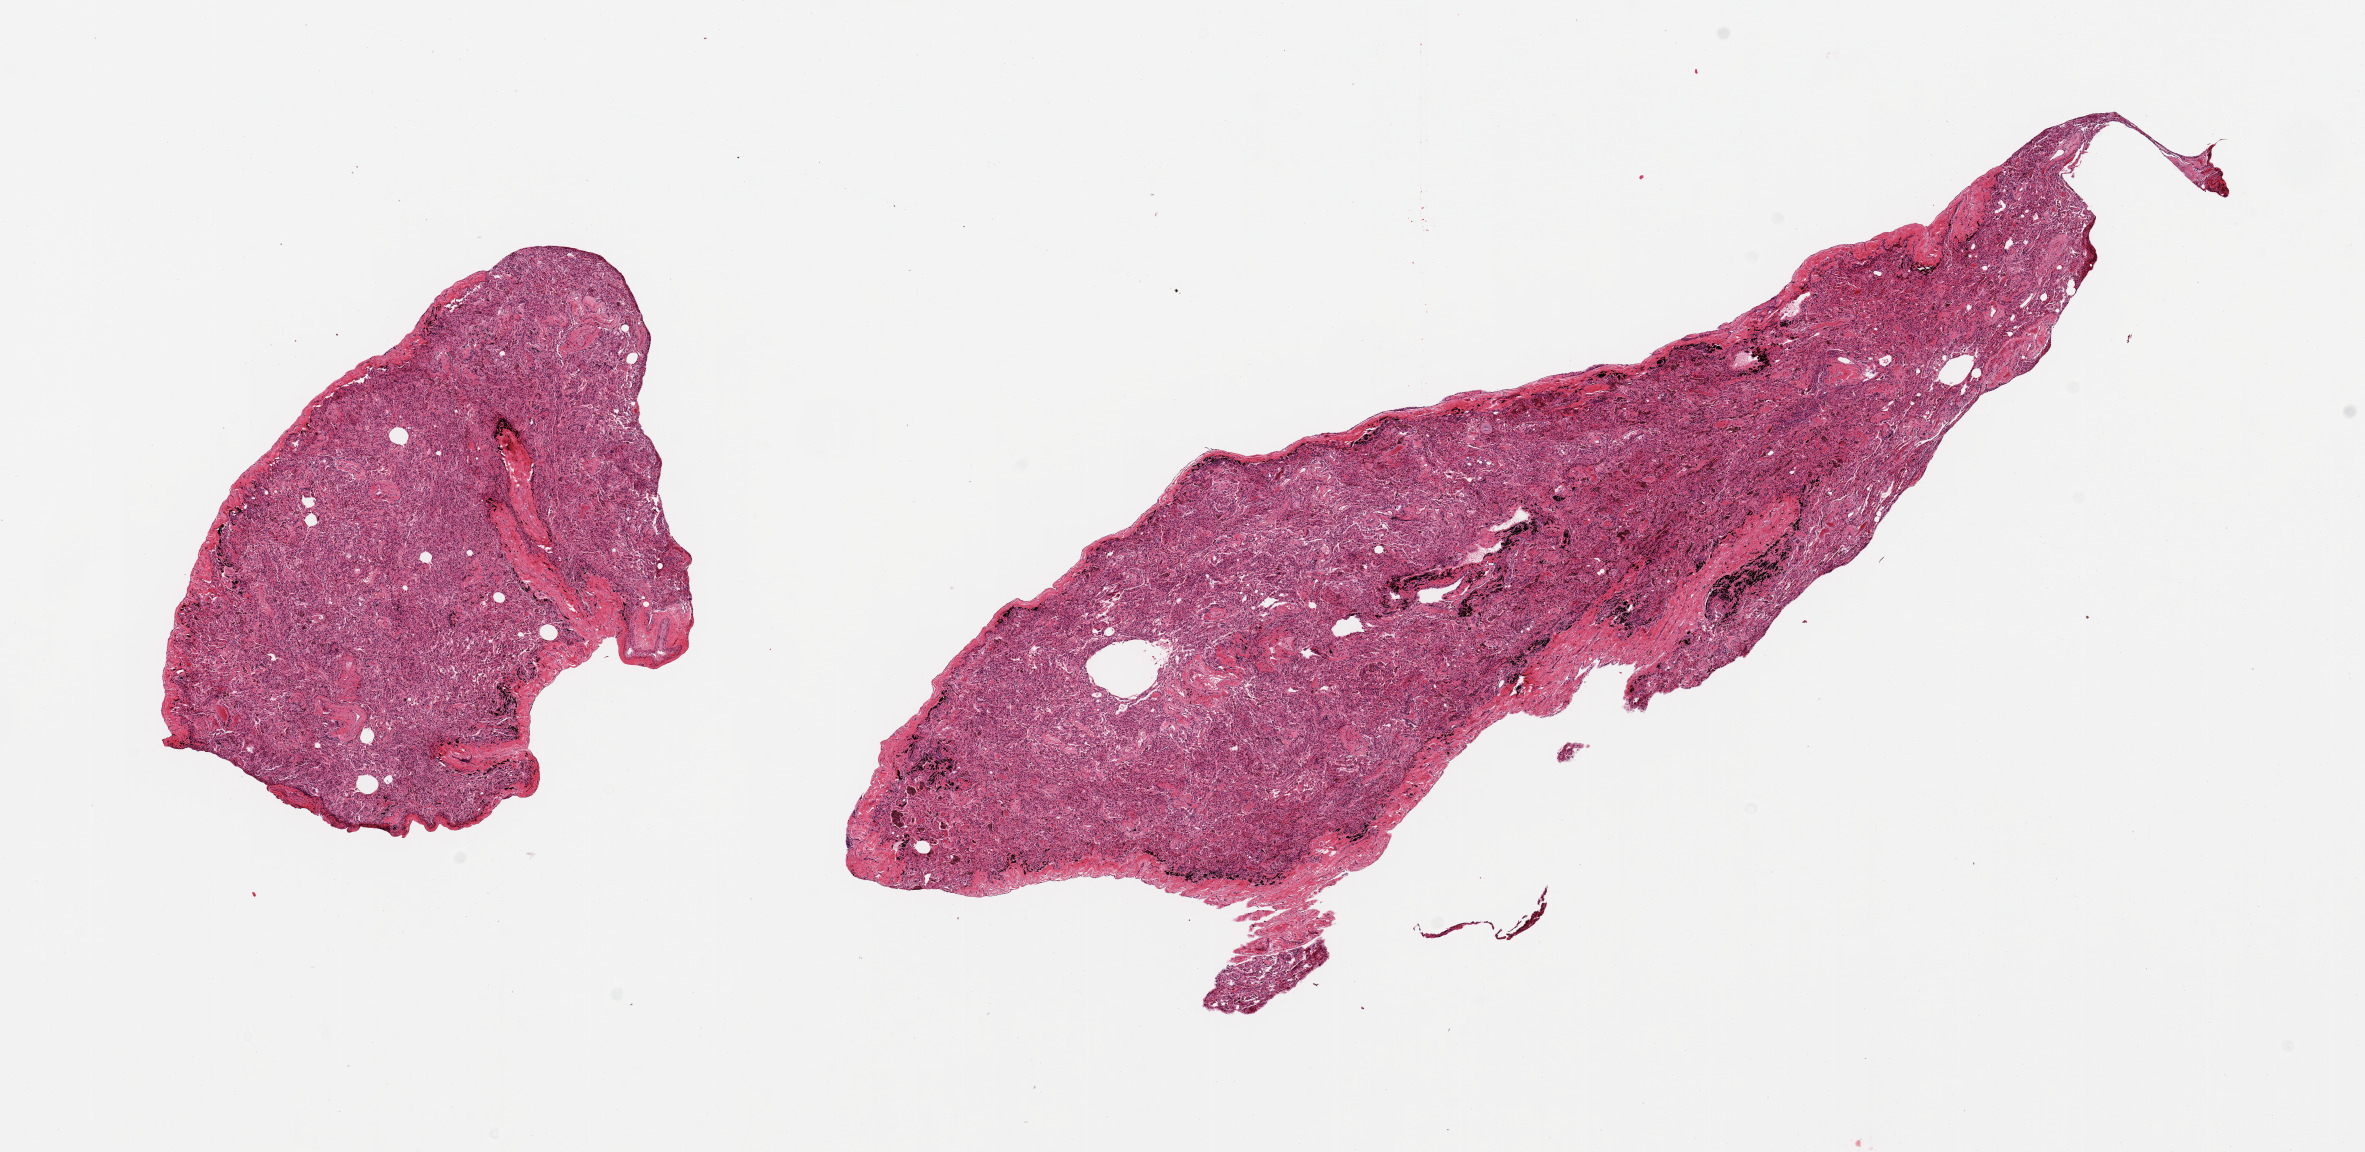
Hematoxylin and eosin (H&E) whole-slide image, whole scanned area (about 18.7 x 9.1 mm, acquisition: 20x scan) shown as a low-resolution overview. PAXgene-fixed paraffin-embedded (PFPE) section. Target tissue: lung. Tissue donor sample. Male donor.
Pathologist's review note for this sample: 2 pieces; atelectatic; moderate anthracotic deposits; pigmented macrophages.